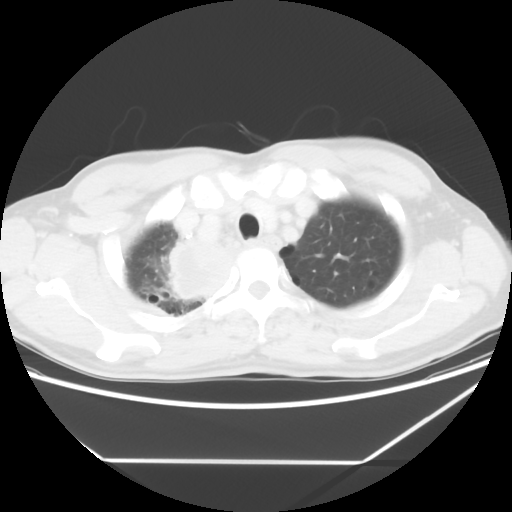
Chest CT, one axial slice; slice 52 of 60 in the series (ordered by position); reconstruction kernel STANDARD; 120 kVp; lung window (W 1500 / L -600 HU); 5 mm slice thickness; 512 × 512 image matrix, field of view 367 × 367 mm. Patient: male, 58 years. From the clinical record (not read from this slice): clinical TNM (as recorded): T2 N2 M0.
Outlined on this slice (bounding box drawn by a radiologist):
- lung tumour (recorded histology: squamous cell carcinoma): bounding box (x1, y1, x2, y2) in pixels: (159, 233, 235, 308)